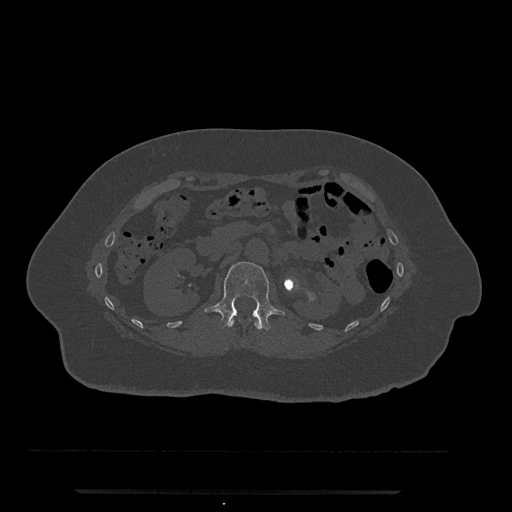
CT including the spine, one axial slice. Slice 116 of 797 in the series (ordered by position). 120 kVp. Bone window (W 1800 / L 400 HU). 0.5 mm slice thickness. 512 × 512 image matrix, field of view 440 × 440 mm. Female patient, age 51 years. Case-level facts recorded for this patient, not image findings: primary cancer: neuro.
Outlined on this slice (semi-automatic segmentation, software-assisted and operator-edited):
- L1 vertebra: bounding box <205,261,285,331> (left, top, right, bottom; pixels)
- T12 vertebra: <230,318,261,330>